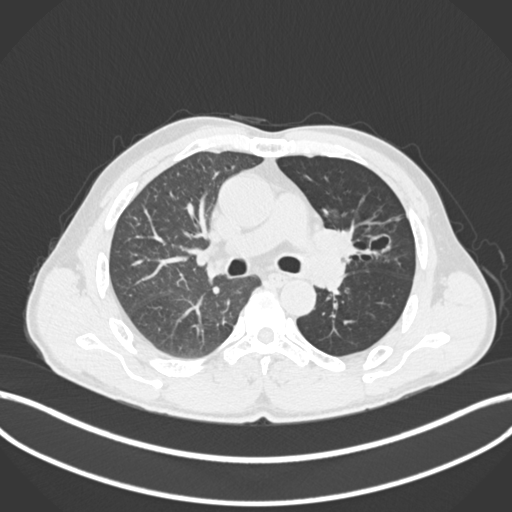
Chest CT, one axial slice. Slice 115 of 255 in the series (ordered by position). Reconstruction kernel B30f. 120 kVp. Lung window (W 1500 / L -600 HU). 1 mm slice thickness. 512 × 512 image matrix, field of view 400 × 400 mm. Male patient, age 57 years. From the clinical record (not read from this slice): clinical TNM (as recorded): T2b N0 M0.
Annotated regions visible in this slice (rectangle marked by the reading radiologist):
- lung tumour (recorded histology: squamous cell carcinoma): bounding box [x1, y1, x2, y2] px = [315, 220, 373, 261]